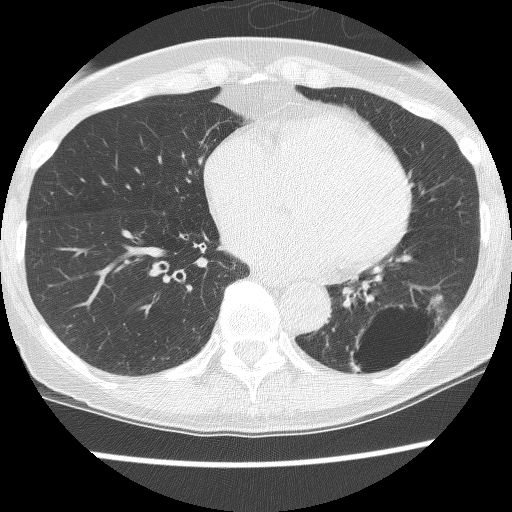
Chest CT (low-dose screening protocol), one axial image. Third screening round (two years after baseline). Lung window (W 1500 / L -600 HU). 2.5 mm slice thickness. Lung (sharp) reconstruction kernel (BONE). Slice 82 of 130 in the series. 512 × 512 image matrix. Female participant, aged 61 years at enrolment. Current smoker at enrolment.
Expert-annotated lung lesion, bounding box [x1, y1, x2, y2] px = [330, 290, 450, 391]. The screening reader recorded 2 non-calcified nodules or masses ≥4 mm on this exam (left lower lobe, left lower lobe); which of them this box marks is not recorded.